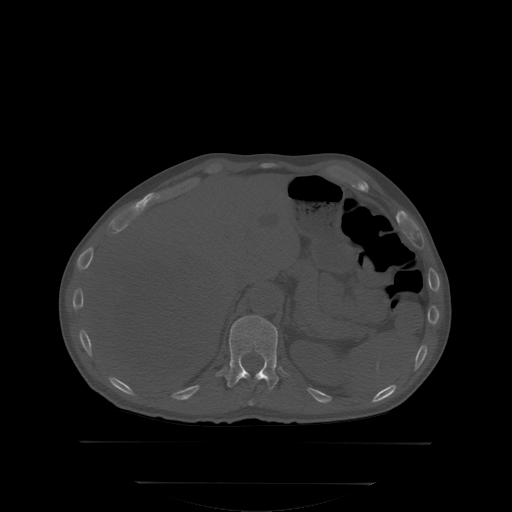
CT including the spine, one axial slice. Position 170 of 350 along the scan axis. Bone window (W 1800 / L 400 HU). 512 × 512 image matrix, field of view 500 × 500 mm. Patient: male, 58 years. From the clinical record (not read from this slice): primary cancer: prostate; vertebrae with lytic lesions (as recorded): L1.
Structures marked on this image (semi-automatically segmented with operator editing):
- T11 vertebra: bounding box <249,400,253,405> (left, top, right, bottom; pixels)
- T12 vertebra: <227,315,278,387>